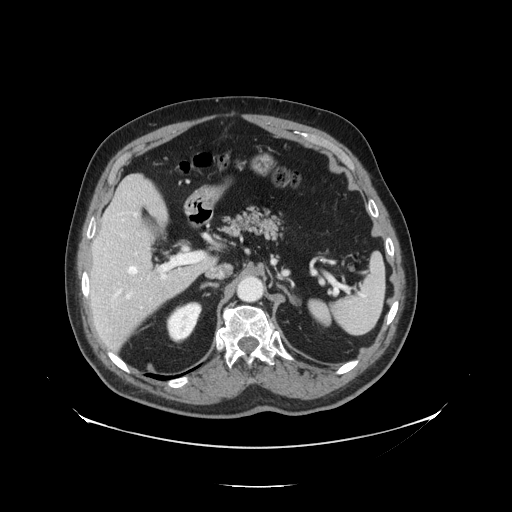
Contrast-enhanced abdominal CT, one axial slice; position 84 of 138 along the scan axis; intravenous contrast given; soft-tissue window (W 400 / L 40 HU); 2.5 mm slice thickness; 512 × 512 image matrix, field of view 497 × 497 mm. Male patient, age 77 years. From the clinical record (not read from this slice): diagnosis: colorectal cancer liver metastases, imaged before liver resection; multiple liver metastases: no; largest metastasis: 1.5 cm; disease in both lobes: no.
Outlined on this slice (expert manual segmentation):
- hepatic veins: bounding box <128,266,138,274> (left, top, right, bottom; pixels)
- liver: <90,176,213,352>
- planned liver remnant (the part of the liver to remain after resection): <91,176,168,287>
- portal vein (with intrahepatic branches): <126,253,205,299>